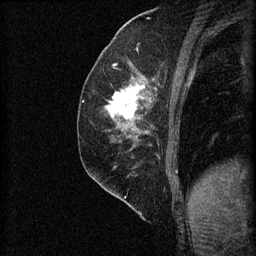
Breast MRI (dynamic contrast-enhanced), one sagittal slice; slice 28 of 60 in the series (ordered by position); 3 images stored at this slice position (order not interpretable as contrast timing); 1.5 T; TE 4.2 ms, TR 8.2 ms; 2 mm slice thickness; 256 × 256 image matrix, field of view 180 × 180 mm. Female patient, age 59 years.
Outlined on this slice (semi-automatic segmentation, software-assisted and operator-edited):
- analysis volume of interest (the breast-tissue region the enhancement analysis was run in; not a lesion): bounding box <105,74,155,131> (left, top, right, bottom; pixels)
- tumour enhancement mask (voxels above the 70 % enhancement threshold inside the analysis volume of interest): <106,86,146,119>